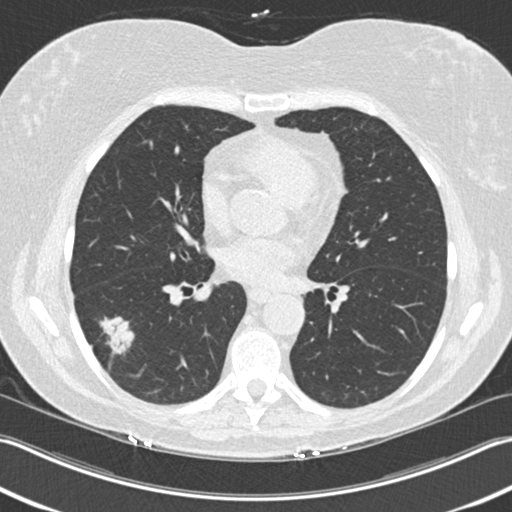
Chest CT (low-dose screening protocol), one axial image. Baseline annual screen. Lung window (W 1500 / L -600 HU). Female participant, aged 63 years at enrolment. Current smoker at enrolment.
Expert reader's lesion annotation, bounding box [x1, y1, x2, y2] px = [75, 312, 138, 370]. The screening reader recorded 3 non-calcified nodules or masses ≥4 mm on this exam (right upper lobe, right lower lobe, right lower lobe); which of them this box marks is not recorded. Later outcome: lung cancer diagnosed 57 days after this screen — bronchiolo-alveolar adenocarcinoma, NOS, right lower lobe, well differentiated (G1), stage IA (AJCC 6th edition), 25 mm at pathology.